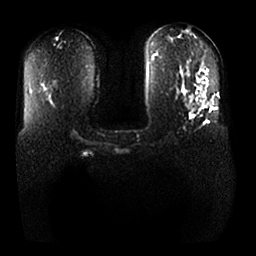
Breast MRI, one axial slice; slice 16 of 25 in the series (ordered by position); diffusion-weighted series; image 2 of 4 stored at this slice position (different b-values; order by instance number); 1.5 T; 256 × 256 image matrix. Female patient.
Annotated regions visible in this slice (expert manual segmentation):
- tumour on diffusion-weighted imaging: bounding box (x1, y1, x2, y2) in pixels: (186, 98, 207, 108)